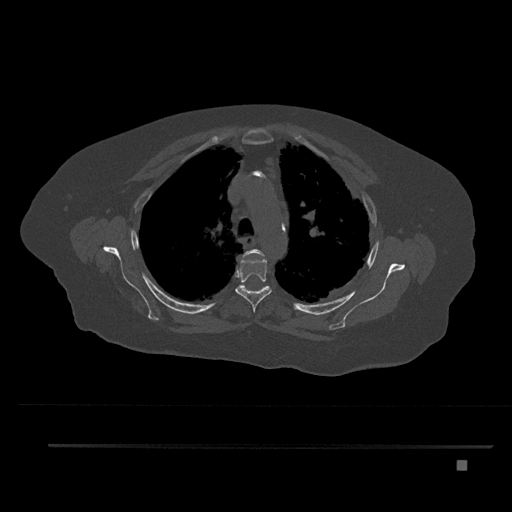
CT including the spine, one axial slice. Position 602 of 797 along the scan axis. Bone window (W 1800 / L 400 HU). 512 × 512 image matrix, field of view 437 × 437 mm. Patient: female, 76 years. From the clinical record (not read from this slice): primary cancer: lung; vertebrae with lytic lesions (as recorded): T11, L3.
Structures marked on this image (semi-automatic segmentation, software-assisted and operator-edited):
- T3 vertebra: bounding box [x1, y1, x2, y2] px = [242, 249, 264, 258]
- T4 vertebra: [235, 255, 272, 312]
- T5 vertebra: [245, 287, 264, 292]